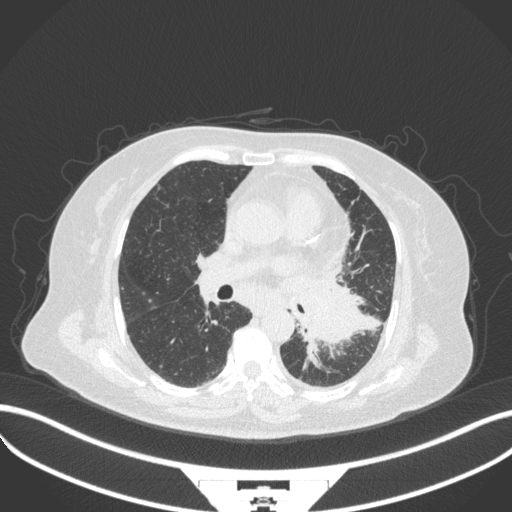
Chest CT, one axial slice. Reconstruction kernel B31f. 120 kVp. Lung window (W 1500 / L -600 HU). 1 mm slice thickness. 512 × 512 image matrix, field of view 400 × 400 mm. Patient: female, 69 years. Case-level facts recorded for this patient, not image findings: clinical TNM (as recorded): T2b N3 M1.
Outlined on this slice (bounding box drawn by a radiologist):
- lung tumour (recorded histology: adenocarcinoma): bounding box [x1, y1, x2, y2] px = [288, 280, 364, 351]